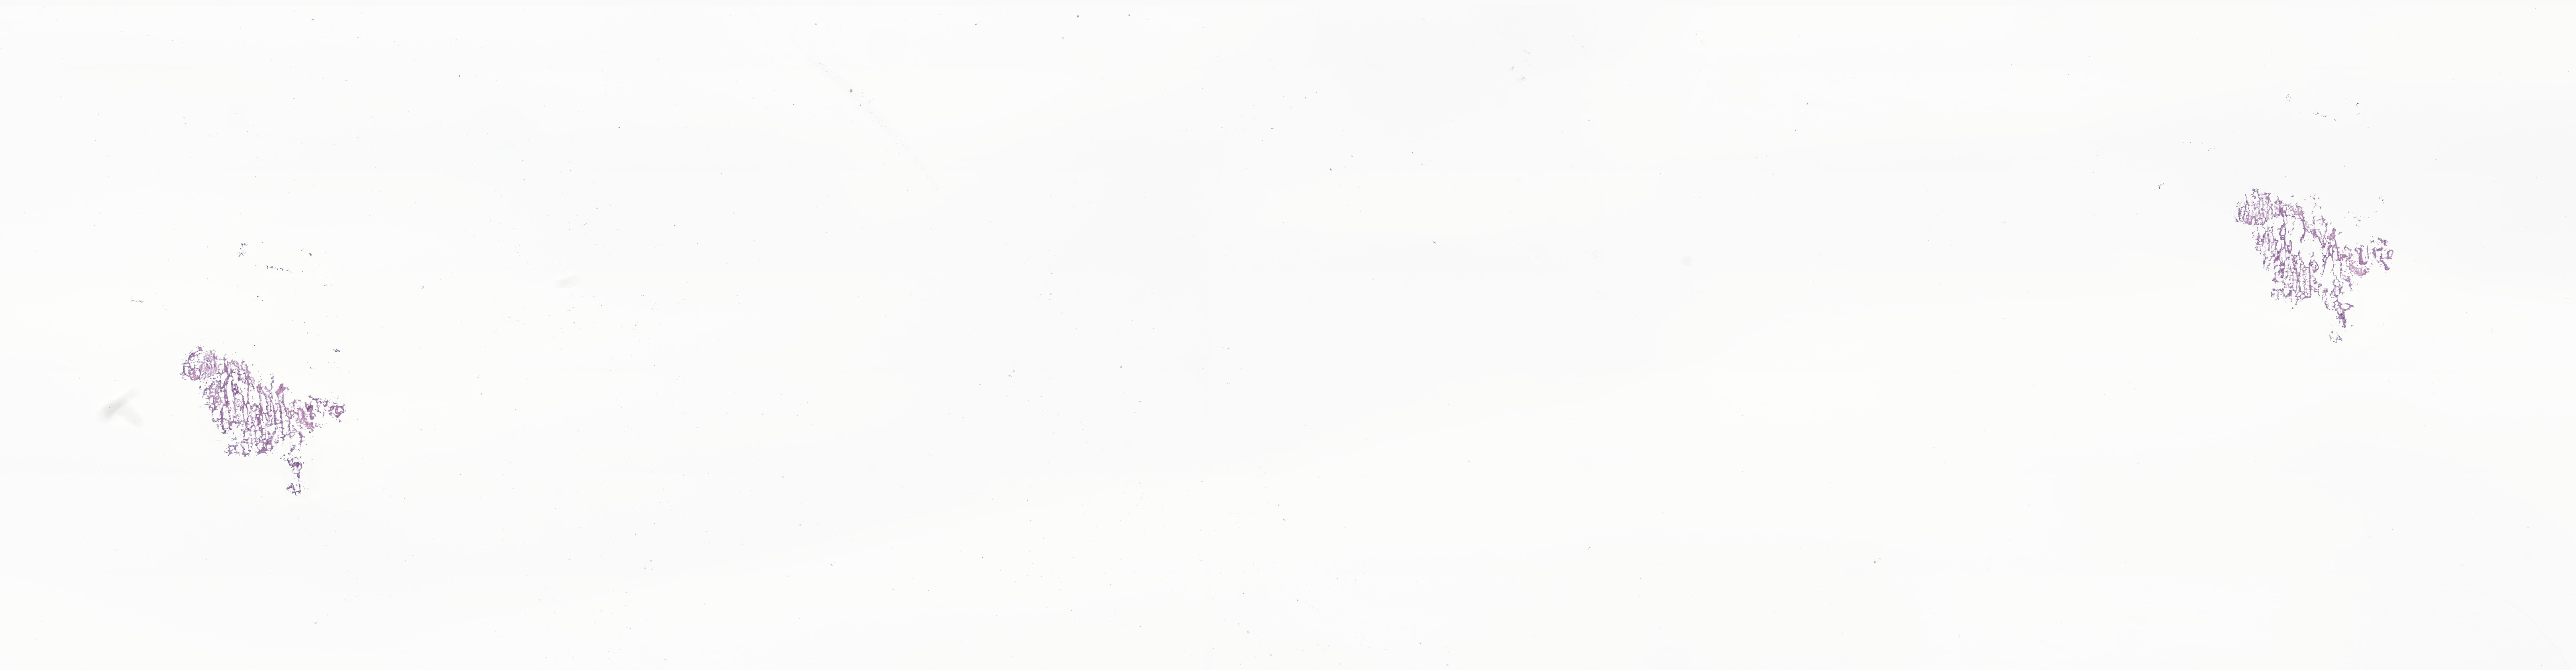
Whole-slide image, haematoxylin and eosin stain of tumor tissue from the brain — whole scanned area (about 27.3 x 7.1 mm) shown as a low-resolution overview; cryosection (OCT / tissue freezing medium). Patient female; age 851 days (about 2.3 years).
- diagnosis (ICD-O-3 morphology term): Neoplasm, uncertain whether benign or malignant